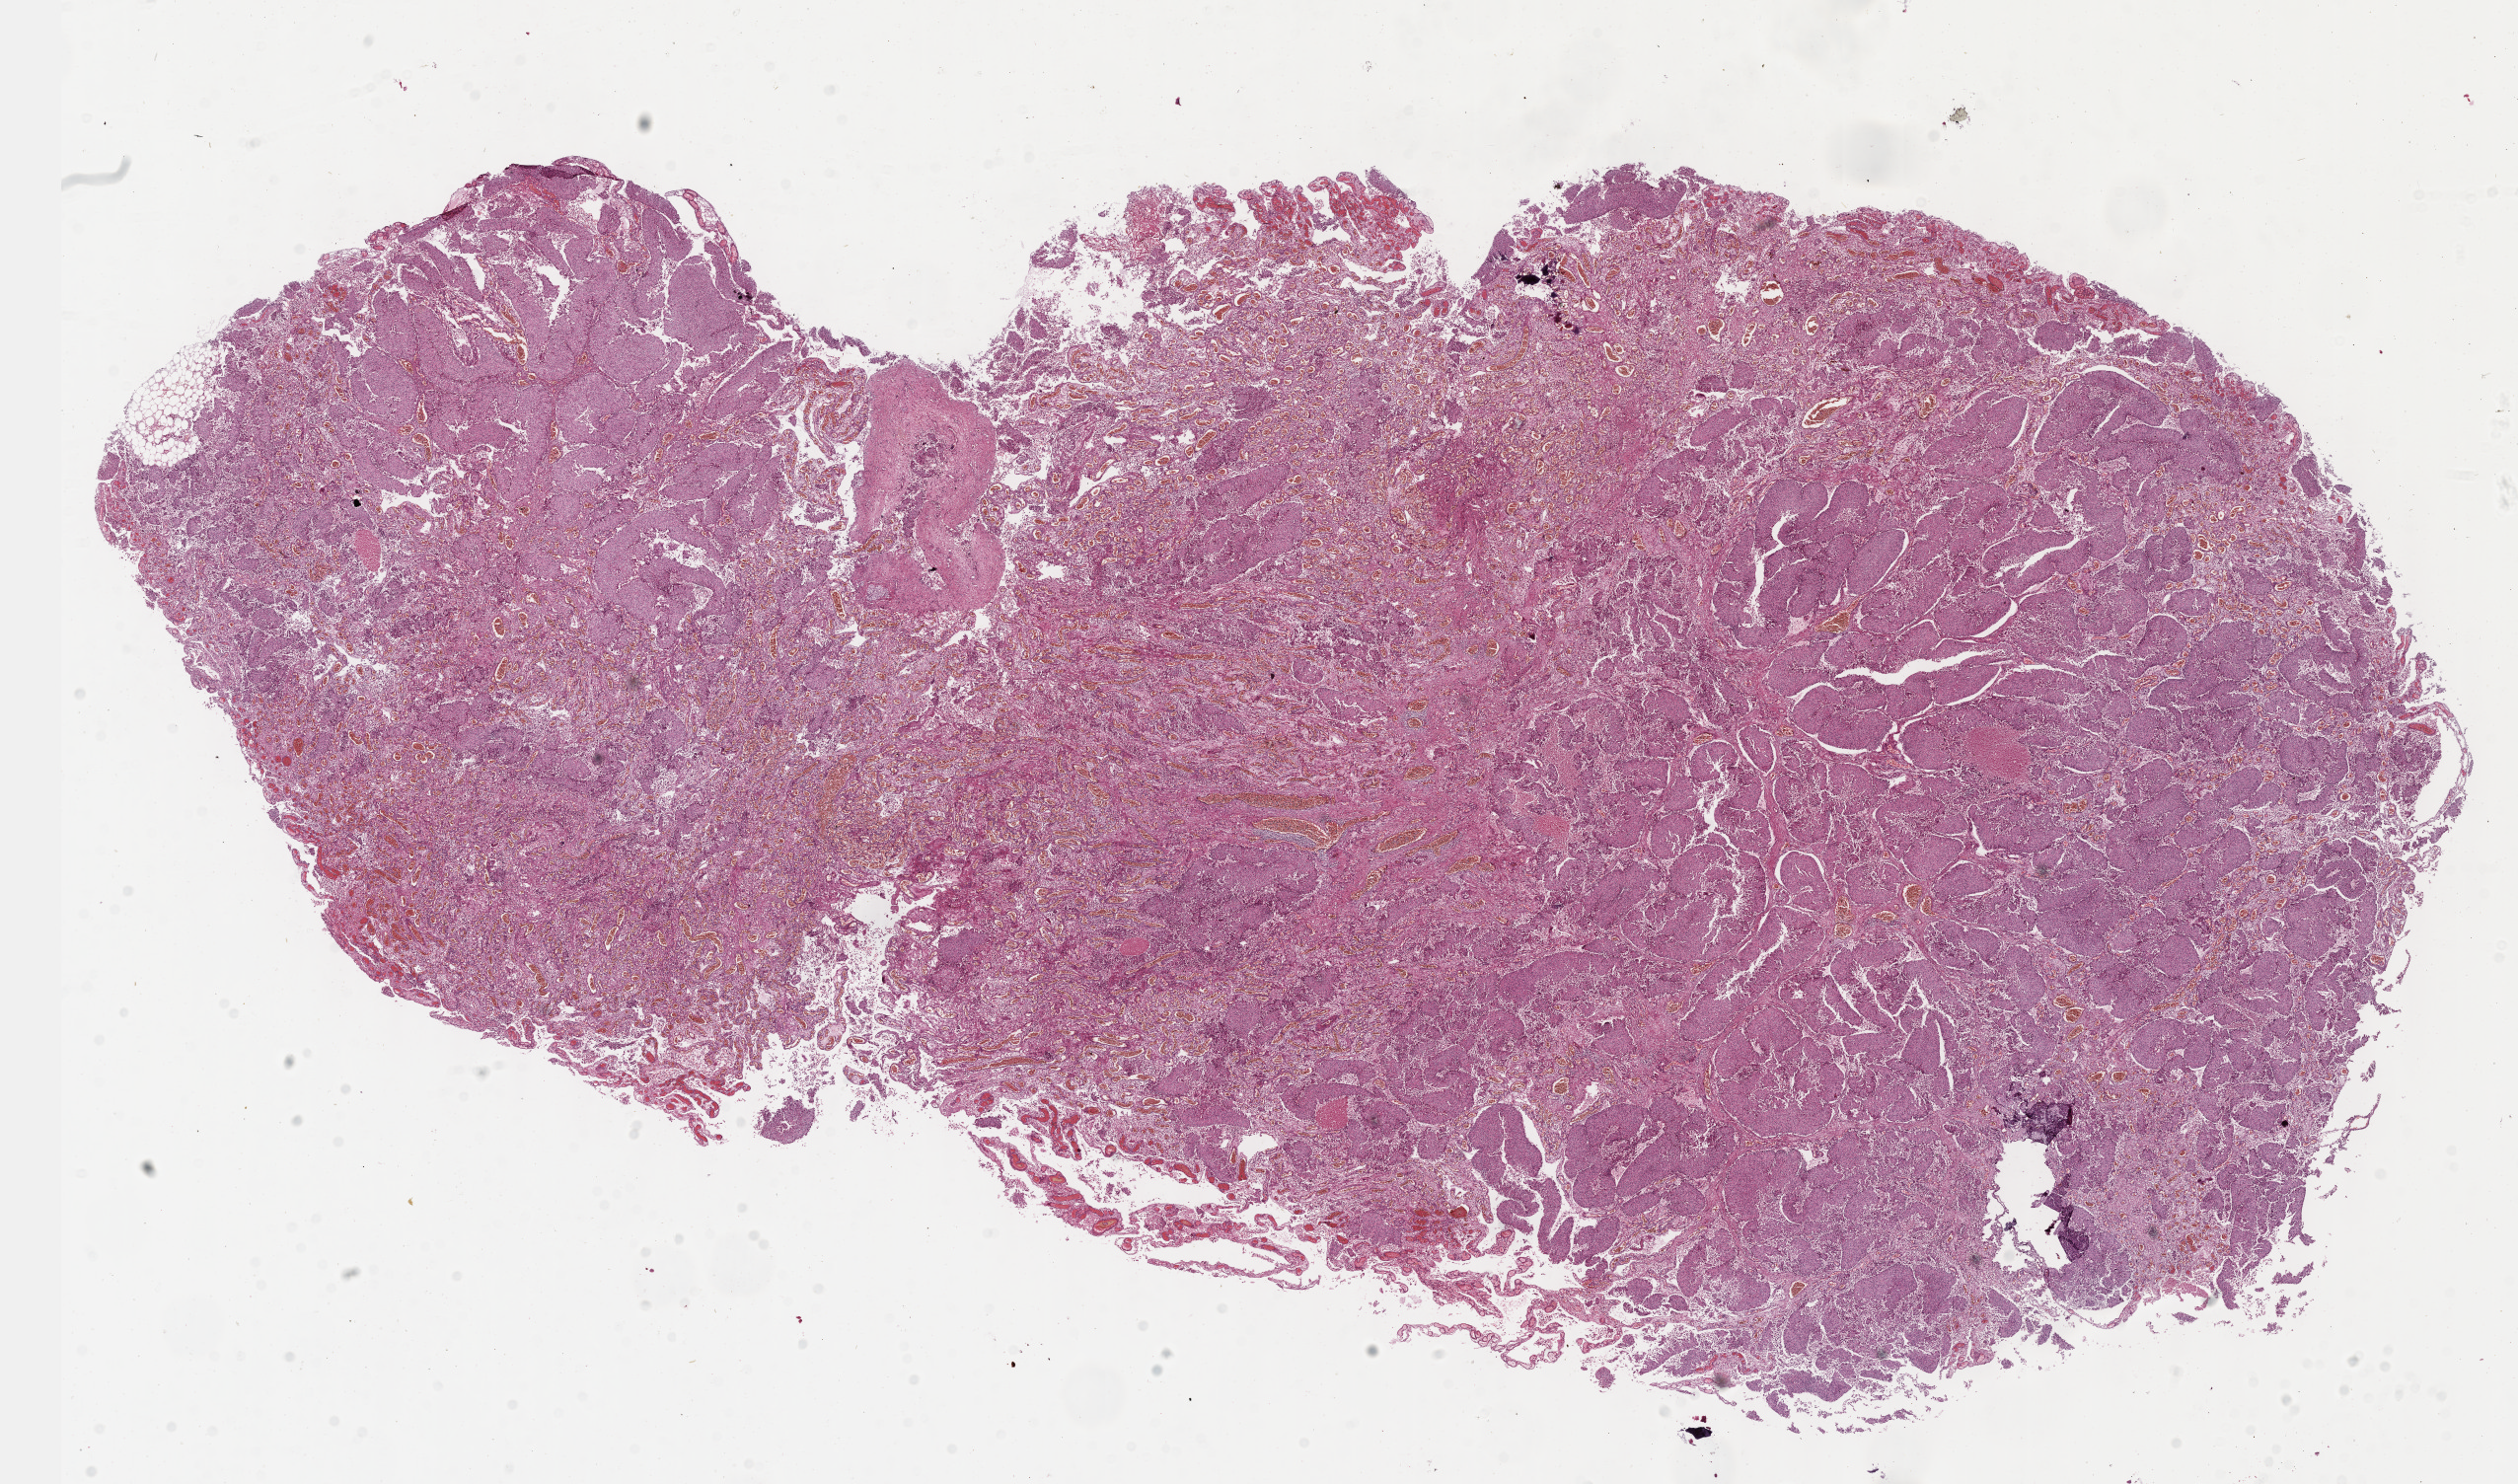
H&E whole-slide image — shown as a low-resolution overview of the whole scanned area (about 20.6 x 12.2 mm). Formalin-fixed paraffin-embedded (FFPE) diagnostic section. Primary tumour sample from the bladder. Male patient; age at initial diagnosis 54 years. Histologic grade: low grade.
• AJCC pathologic stage: II
• pathologic diagnosis: Papillary transitional cell carcinoma (lateral wall of bladder)